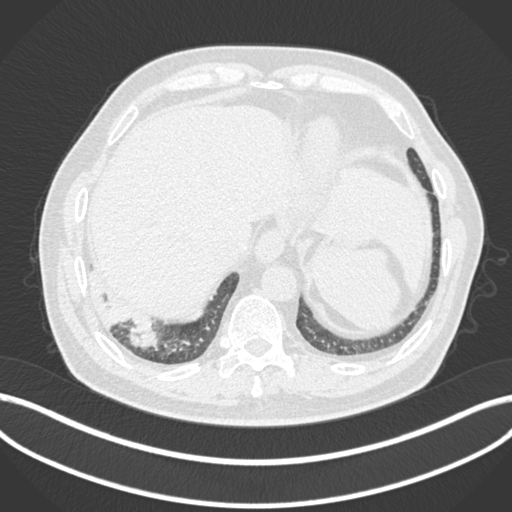
Chest CT, one axial slice; slice 18 of 200 in the series (ordered by position); lung window (W 1500 / L -600 HU); 1 mm slice thickness; 512 × 512 image matrix, field of view 400 × 400 mm. Male patient, age 59 years.
Outlined on this slice (bounding box drawn by a radiologist):
- lung tumour (recorded histology: adenocarcinoma): box from (x=128, y=316) to (x=161, y=355) px